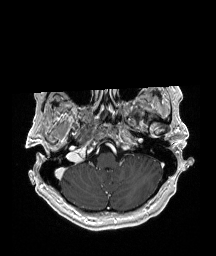
Brain MRI from a brain-tumour surgery series, one axial slice. Position 153 of 192 along the scan axis. T1-weighted post-contrast. 1 mm slice thickness. 216 × 256 image matrix. From the clinical record (not read from this slice): histopathology: Glioblastoma; WHO grade: 4; IDH mutation: no.
Annotated regions visible in this slice (outlined manually by an expert reader):
- previous resection cavity: box from (x=129, y=114) to (x=139, y=122) px